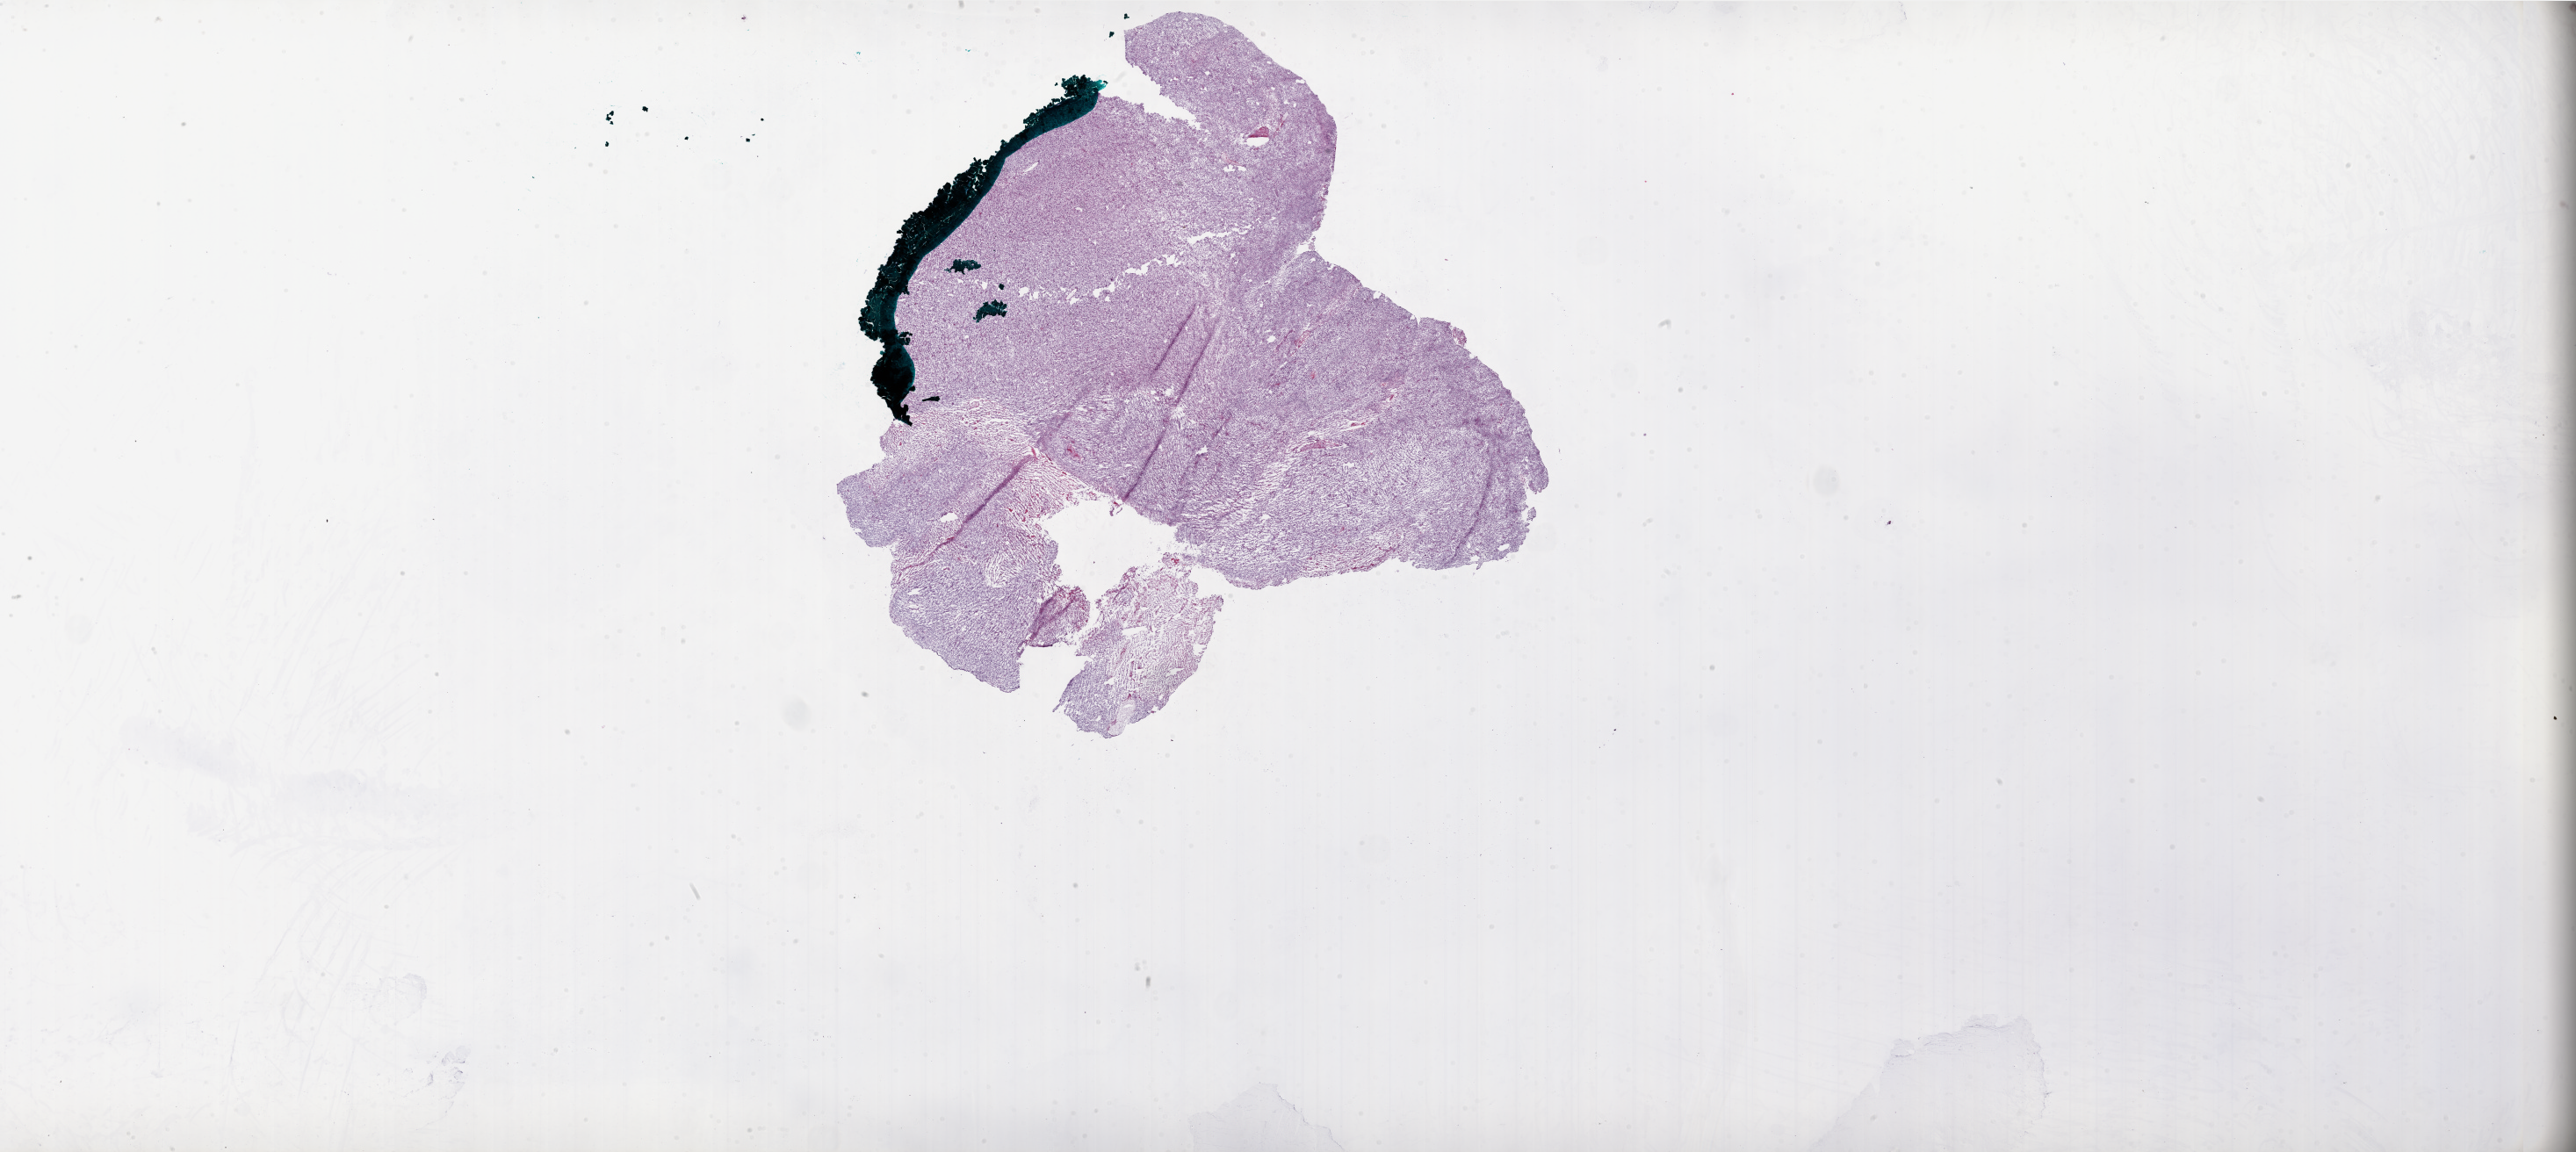
Whole-slide histology image, H&E-stained, shown as a low-resolution overview of the whole scanned area (about 47.0 x 21.0 mm, acquisition: 20x scan), frozen section from the bottom of the tissue portion, primary tumour sample from the brain. Patient: female, age at initial diagnosis 67 years. Composition of this section per pathologist review: tumour cells 95%, tumour nuclei 100%, normal cells 0%, stromal cells 0%, necrosis 5%.
* pathologic diagnosis: Glioblastoma